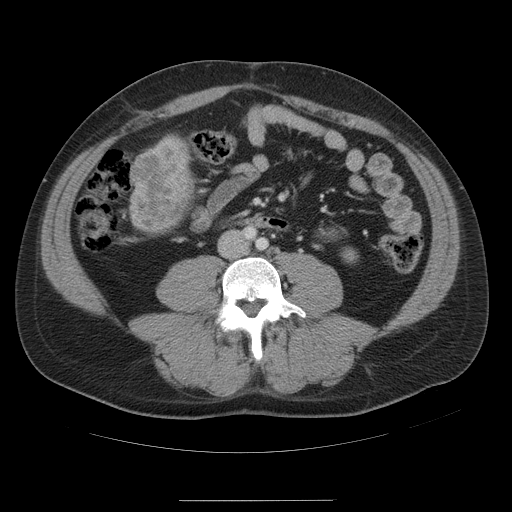
Contrast-enhanced abdominal CT, one axial slice. Position 6 of 54 along the scan axis. Intravenous contrast given. Soft-tissue window (W 400 / L 40 HU). 5 mm slice thickness. 512 × 512 image matrix, field of view 436 × 436 mm. Male patient, age 40 years. From the clinical record (not read from this slice): diagnosis: colorectal cancer liver metastases, imaged before liver resection; multiple liver metastases: no; largest metastasis: 15 cm; chemotherapy before resection: no.
Outlined on this slice (manually delineated by an expert):
- liver: bounding box <129,137,193,233> (left, top, right, bottom; pixels)
- liver metastasis: <132,144,188,227>